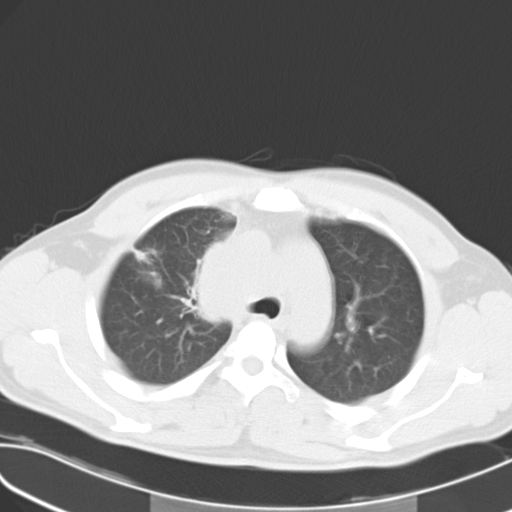
Chest CT, one axial slice. Position 20 of 27 along the scan axis. Reconstruction kernel B40f. 120 kVp. Lung window (W 1500 / L -600 HU). 10 mm slice thickness. 512 × 512 image matrix, field of view 346 × 346 mm. Male patient, age 32 years. From the clinical record (not read from this slice): clinical TNM (as recorded): T4 N3 M0; histopathological grade: G3.
Outlined on this slice (rectangle marked by the reading radiologist):
- lung tumour (recorded histology: small cell carcinoma): box from (x=187, y=235) to (x=237, y=329) px